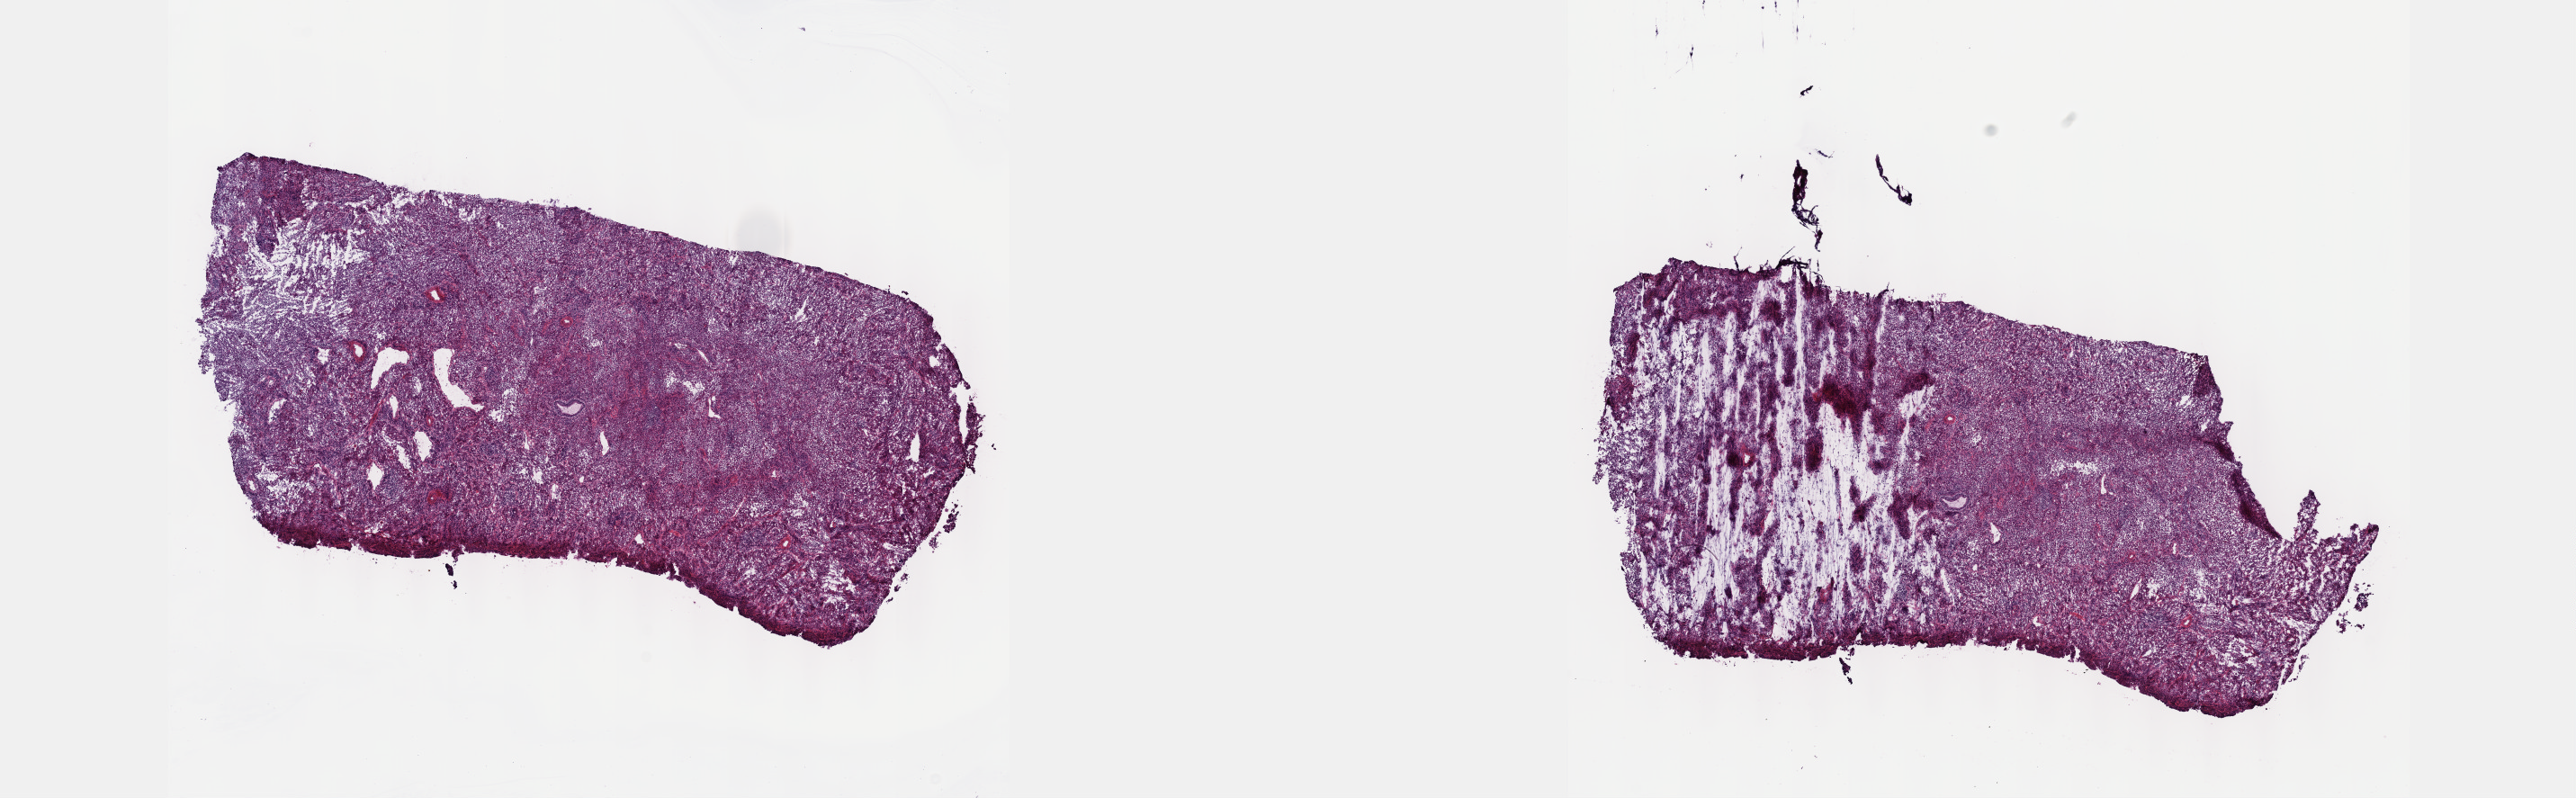
H&E-stained whole-slide image — a low-resolution overview of the entire scanned area, about 23.1 x 7.2 mm. Frozen section. Sample: primary tumour, cervix. Female, age 38 years at initial diagnosis. Histologic grade: G2 (moderately differentiated). Composition of this section per pathologist review: tumour cells 80%, tumour nuclei 80%, normal cells 0%, stromal cells 20%, necrosis 0%. Infiltration values recorded for this section: lymphocyte infiltration 40%, monocyte infiltration 20%, neutrophil infiltration 20%.
• FIGO stage: IIB
• diagnosis: Squamous cell carcinoma, NOS (cervix uteri)